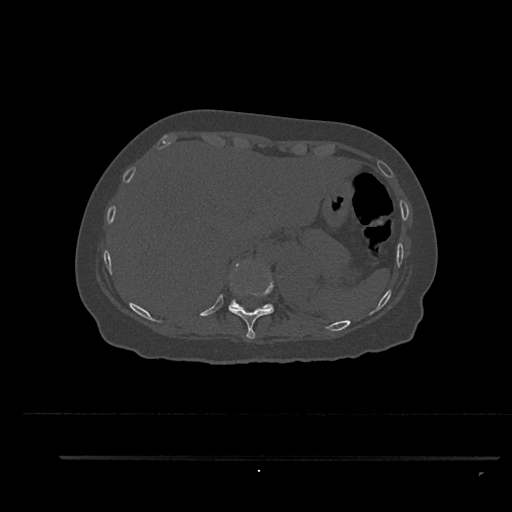
CT including the spine, one axial slice; slice 348 of 797 in the series (ordered by position); reconstruction kernel Br40s/3; 120 kVp; bone window (W 1800 / L 400 HU); 0.5 mm slice thickness; 512 × 512 image matrix. Patient: female, 44 years. From the clinical record (not read from this slice): primary cancer: renal; vertebrae with lytic lesions (as recorded): L1.
Structures marked on this image (semi-automatically segmented with operator editing):
- T10 vertebra: box from (x=228, y=261) to (x=274, y=339) px
- T11 vertebra: (x=229, y=263)–(x=273, y=309)